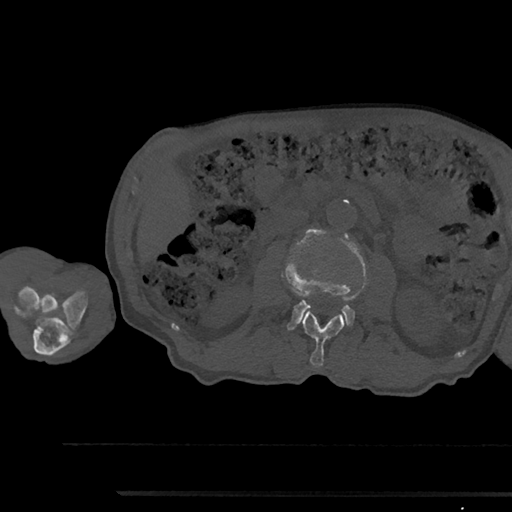
CT including the spine, one axial slice. Position 528 of 797 along the scan axis. Bone window (W 1800 / L 400 HU). 0.5 mm slice thickness. 512 × 512 image matrix. Patient: male, 79 years. Case-level facts recorded for this patient, not image findings: primary cancer: prostate.
Outlined on this slice (semi-automatic segmentation, software-assisted and operator-edited):
- L2 vertebra: bounding box (x1, y1, x2, y2) in pixels: (301, 311, 345, 367)
- L3 vertebra: (284, 230, 367, 330)